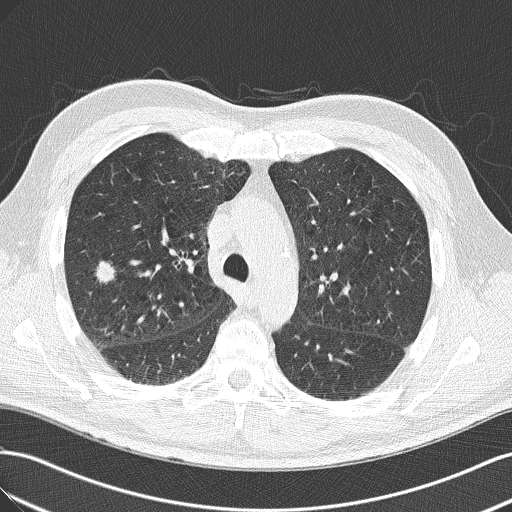
Low-dose screening chest CT, one axial slice. Slice 93 of 143 in the series (ordered by position). Lung window (W 1500 / L -600 HU). 2 mm slice thickness. 512 × 512 image matrix, field of view 360 × 360 mm.
Structures marked on this image (expert manual segmentation):
- lesion 1 (tumor, lower lobe of right lung): box from (x=96, y=261) to (x=115, y=283) px